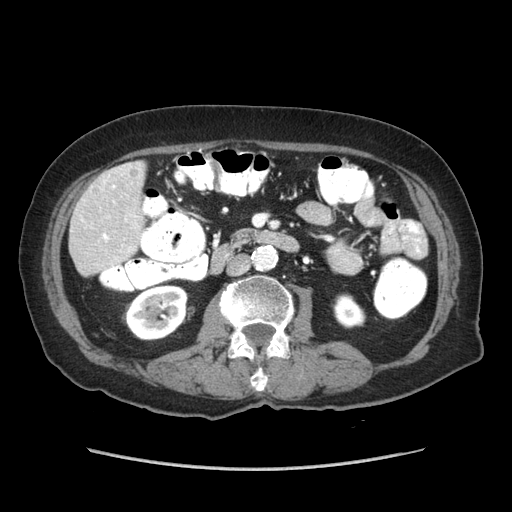
Contrast-enhanced abdominal CT (liver protocol), one axial slice; slice 17 of 89 in the series (ordered by position); soft-tissue window (W 400 / L 40 HU); 2.5 mm slice thickness; 512 × 512 image matrix, field of view 360 × 360 mm. From the clinical record (not read from this slice): diagnosis: hepatocellular carcinoma (patient treated with transarterial chemoembolisation; whether this scan precedes or follows treatment is not stated here); TNM stage (as recorded): Stage-IIIA; Child-Pugh class: A; tumour nodularity: multinodular; tumour size: 11 cm.
Structures marked on this image (semi-automatic segmentation, software-assisted and operator-edited):
- liver parenchyma outside the tumour (the mass and vessels are separate outlines, so this box may not span the whole liver): bounding box [x1, y1, x2, y2] px = [70, 160, 146, 274]
- liver vessels: [103, 181, 131, 251]